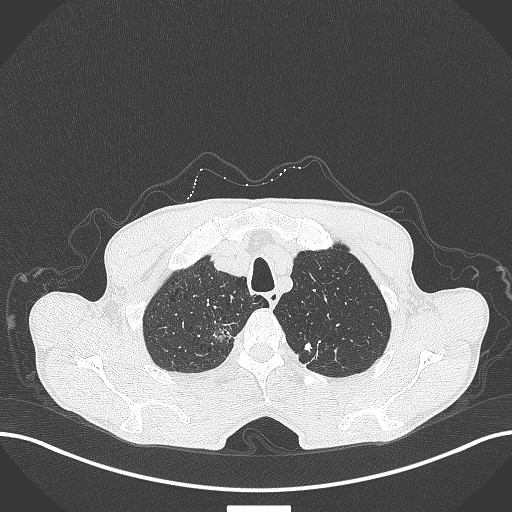
Chest CT, one axial slice. Position 373 of 445 along the scan axis. Reconstruction kernel B70f. 120 kVp. Lung window (W 1500 / L -600 HU). 1 mm slice thickness. 512 × 512 image matrix, field of view 400 × 400 mm. Patient: male, 70 years. From the clinical record (not read from this slice): clinical TNM (as recorded): T1a N0 M0; histopathological grade: G1-2.
Annotated regions visible in this slice (bounding box drawn by a radiologist):
- lung tumour (recorded histology: adenocarcinoma): bounding box [x1, y1, x2, y2] px = [208, 323, 235, 346]